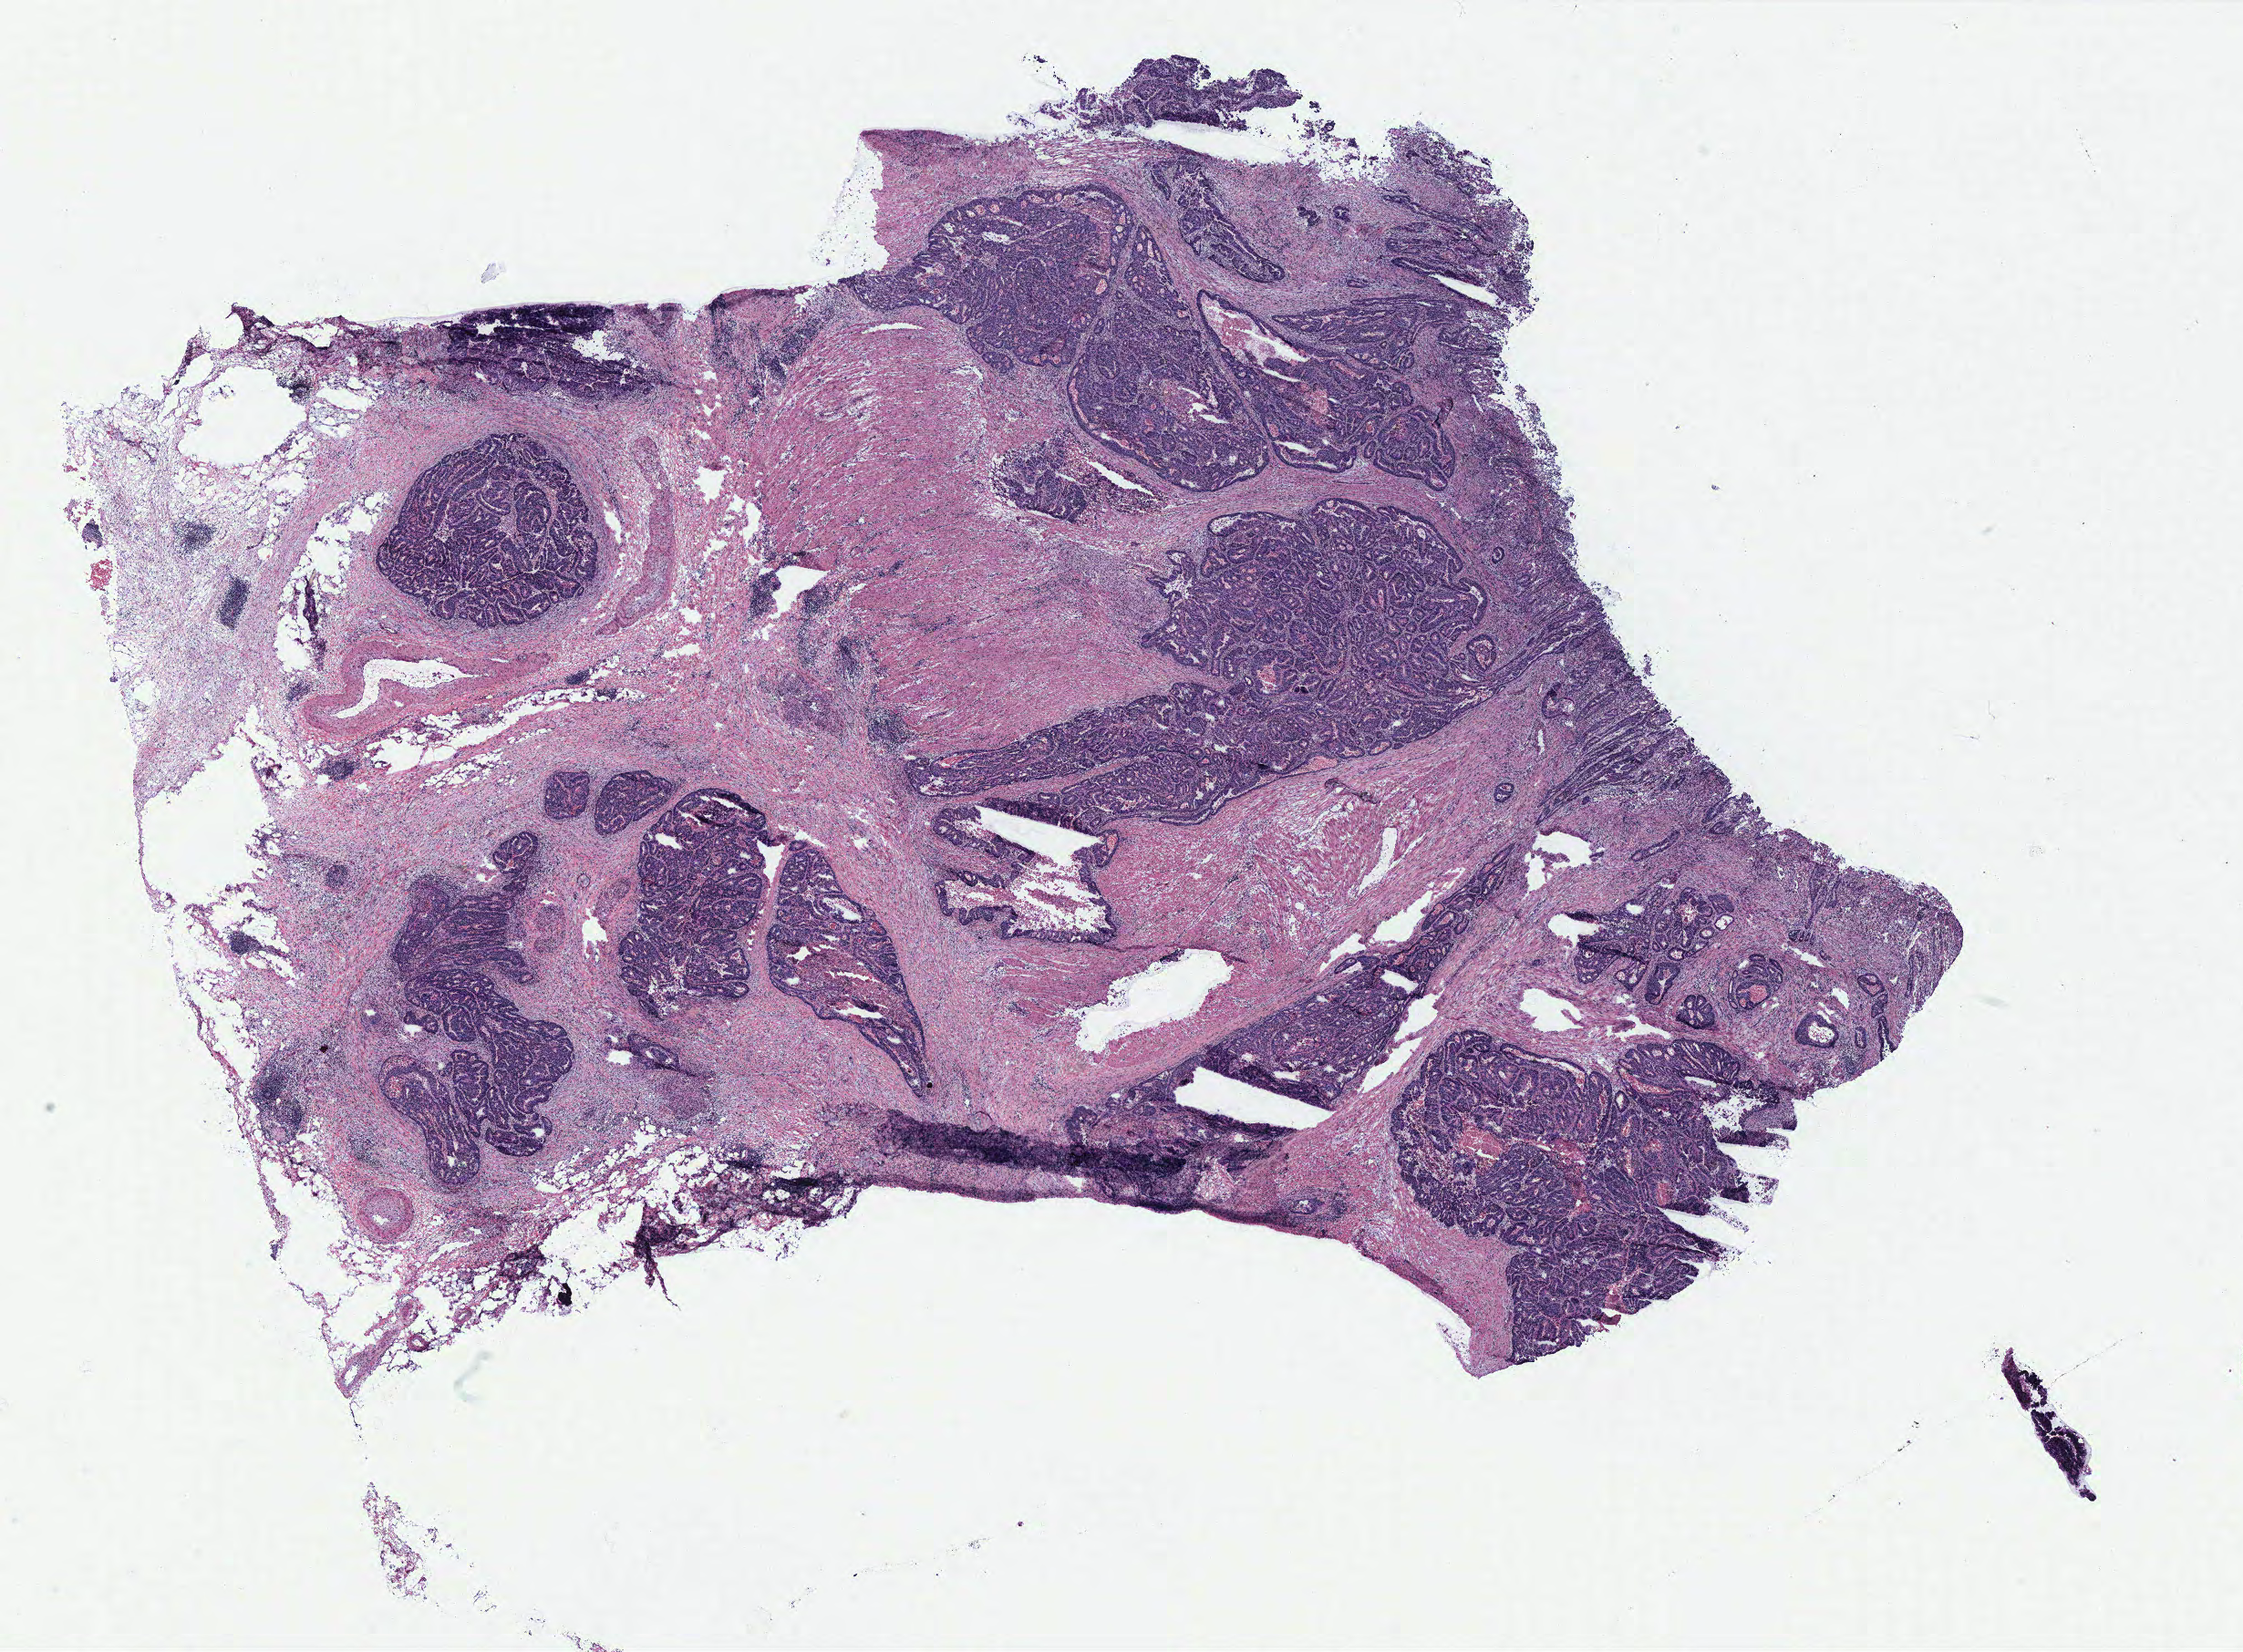
Hematoxylin and eosin (H&E) stained whole-slide image, whole scanned area (about 19.7 x 14.5 mm) shown as a low-resolution overview, colon, tissue type not recorded.
• patient diagnosis (cohort enrolment): colon cancer (colon)